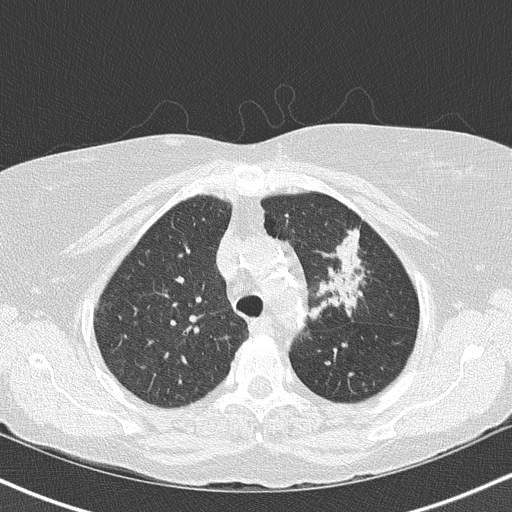
Low-dose screening chest CT, one axial slice. Slice 114 of 147 in the series (ordered by position). Reconstruction kernel B50f. 120 kVp. Lung window (W 1500 / L -600 HU). 2 mm slice thickness. 512 × 512 image matrix.
Annotated regions visible in this slice (expert manual segmentation):
- lesion 1 (tumor, upper lobe of left lung): bounding box (x1, y1, x2, y2) in pixels: (321, 230, 362, 306)